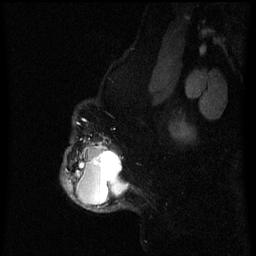
Breast MRI (dynamic contrast-enhanced), one sagittal slice; slice 52 of 60 in the series (ordered by position); dynamic contrast-enhanced series, image 2 of 3 at this slice position (ordered by acquisition); 1.5 T; TE 4.2 ms, TR 8 ms; 2 mm slice thickness; 256 × 256 image matrix. Patient: female, 50 years.
Structures marked on this image (semi-automatic segmentation, software-assisted and operator-edited):
- analysis volume of interest (the breast-tissue region the enhancement analysis was run in; not a lesion): bounding box (x1, y1, x2, y2) in pixels: (61, 136, 128, 213)
- tumour enhancement mask (voxels above the 70 % enhancement threshold inside the analysis volume of interest): (65, 142, 128, 208)